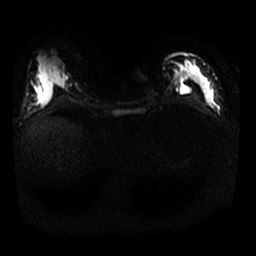
Breast MRI, one axial slice; slice 14 of 25 in the series (ordered by position); diffusion-weighted series; image 2 of 4 stored at this slice position (different b-values; order by instance number); 1.5 T; 4 mm slice thickness; 256 × 256 image matrix, field of view 320 × 320 mm. Female patient.
Structures marked on this image (expert manual segmentation):
- tumour on diffusion-weighted imaging: bounding box (x1, y1, x2, y2) in pixels: (191, 65, 213, 107)